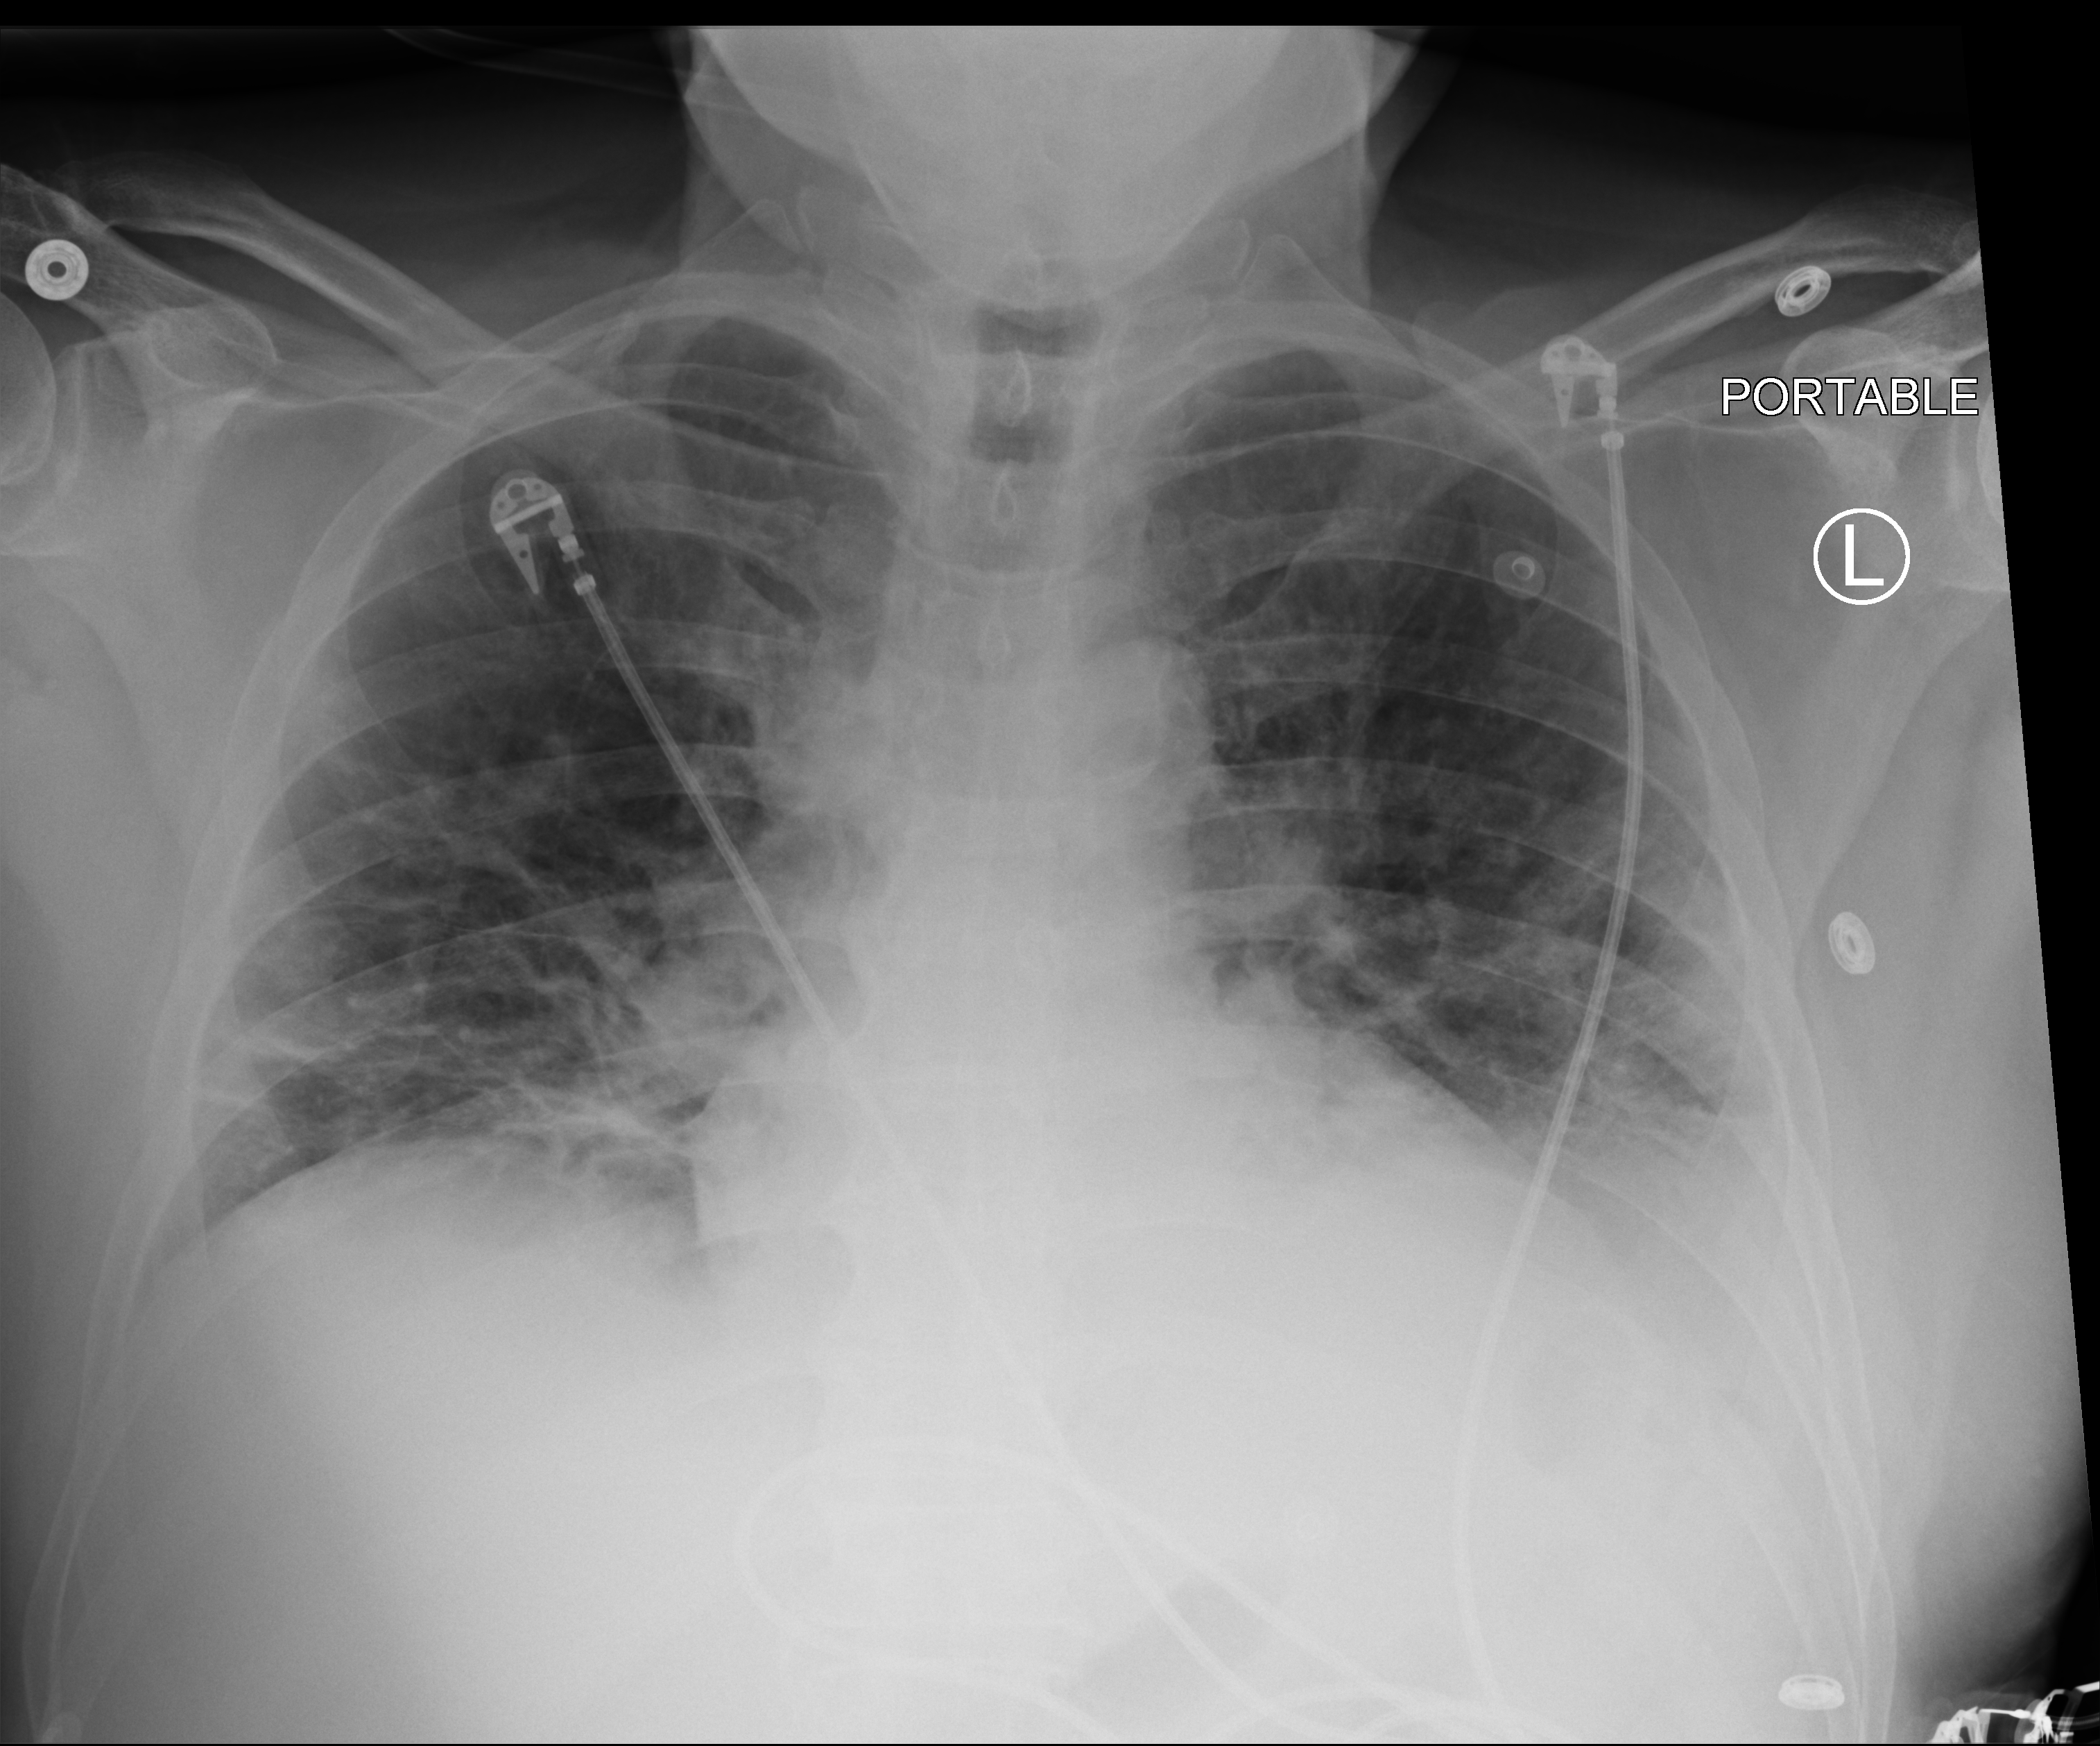
Bedside chest radiograph (computed radiography); anteroposterior (AP) projection. Male patient hospitalised with COVID-19, age 60–74 years.
From the hospital-stay record, not from the radiograph (when in the stay this image was taken is not recorded): chronic kidney disease (admission record): no; smoking status (admission record): former.